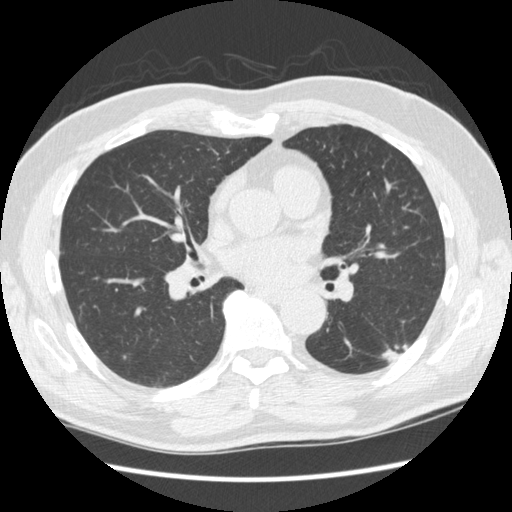
Axial slice from a low-dose chest CT screening exam, baseline screening round, lung window (W 1500 / L -600 HU), 1.25 mm slice thickness, 120 kVp, slice 128 of 267 in the series, 512 × 512 image matrix, field of view 360 × 360 mm. Male, age 74 years at enrolment.
Expert reader's lesion annotation, box from (x=375, y=324) to (x=417, y=373) px. The screening reader recorded 3 non-calcified nodules or masses ≥4 mm on this exam; which of them this box marks is not recorded. Official screen result: positive, change unspecified: nodule(s) >= 4 mm or enlarging nodule(s), mass(es), or other non-specific abnormalities suspicious for lung cancer. Later outcome: lung cancer diagnosed 384 days after this screen (after the second annual screen) — squamous cell carcinoma, NOS, left lower lobe, well differentiated (G1), stage IA (AJCC 6th edition), 28 mm at pathology.